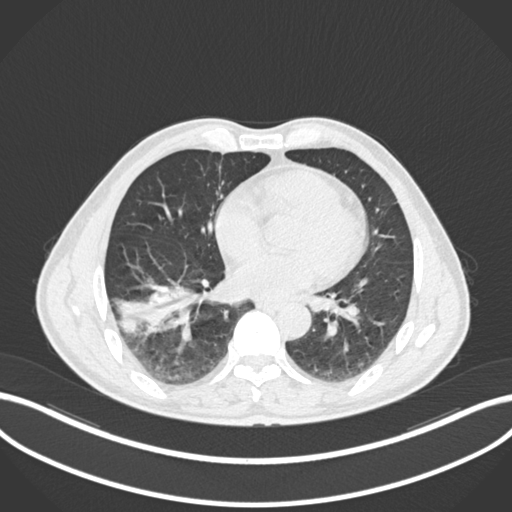
Chest CT, one axial slice. Position 76 of 208 along the scan axis. Reconstruction kernel B30f. 120 kVp. Lung window (W 1500 / L -600 HU). 1 mm slice thickness. 512 × 512 image matrix. Patient: male, 58 years. Case-level facts recorded for this patient, not image findings: clinical TNM (as recorded): T3 N0 M0.
Outlined on this slice (rectangle marked by the reading radiologist):
- lung tumour (recorded histology: squamous cell carcinoma): bounding box [x1, y1, x2, y2] px = [108, 277, 201, 339]